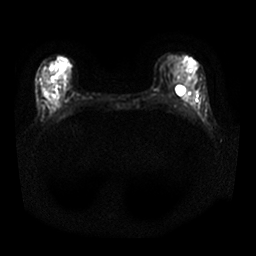
Breast MRI, one axial slice. Position 10 of 25 along the scan axis. Diffusion-weighted series; image 2 of 4 stored at this slice position (different b-values; order by instance number). 1.5 T. 4 mm slice thickness. 256 × 256 image matrix. Female patient.
Annotated regions visible in this slice (manually delineated by an expert):
- tumour on diffusion-weighted imaging: bounding box <40,83,42,85> (left, top, right, bottom; pixels)